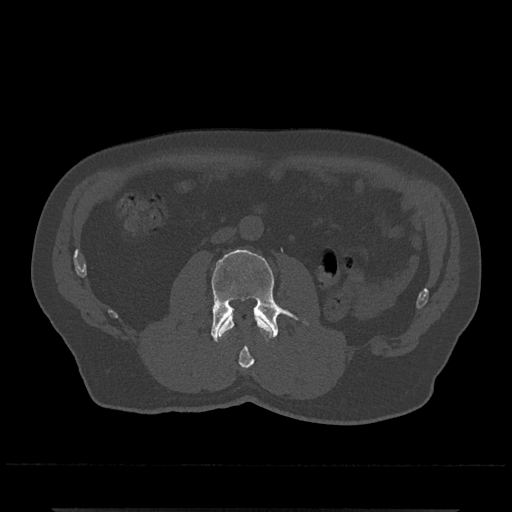
CT including the spine, one axial slice. Slice 242 of 797 in the series (ordered by position). Reconstruction kernel Br40s/3. 120 kVp. Bone window (W 1800 / L 400 HU). 0.5 mm slice thickness. 512 × 512 image matrix, field of view 393 × 393 mm. Patient: male, 67 years. Case-level facts recorded for this patient, not image findings: primary cancer: prostate.
Structures marked on this image (semi-automatic segmentation, software-assisted and operator-edited):
- L2 vertebra: box from (x=219, y=315) to (x=271, y=369) px
- L3 vertebra: (x=211, y=249)–(x=309, y=342)